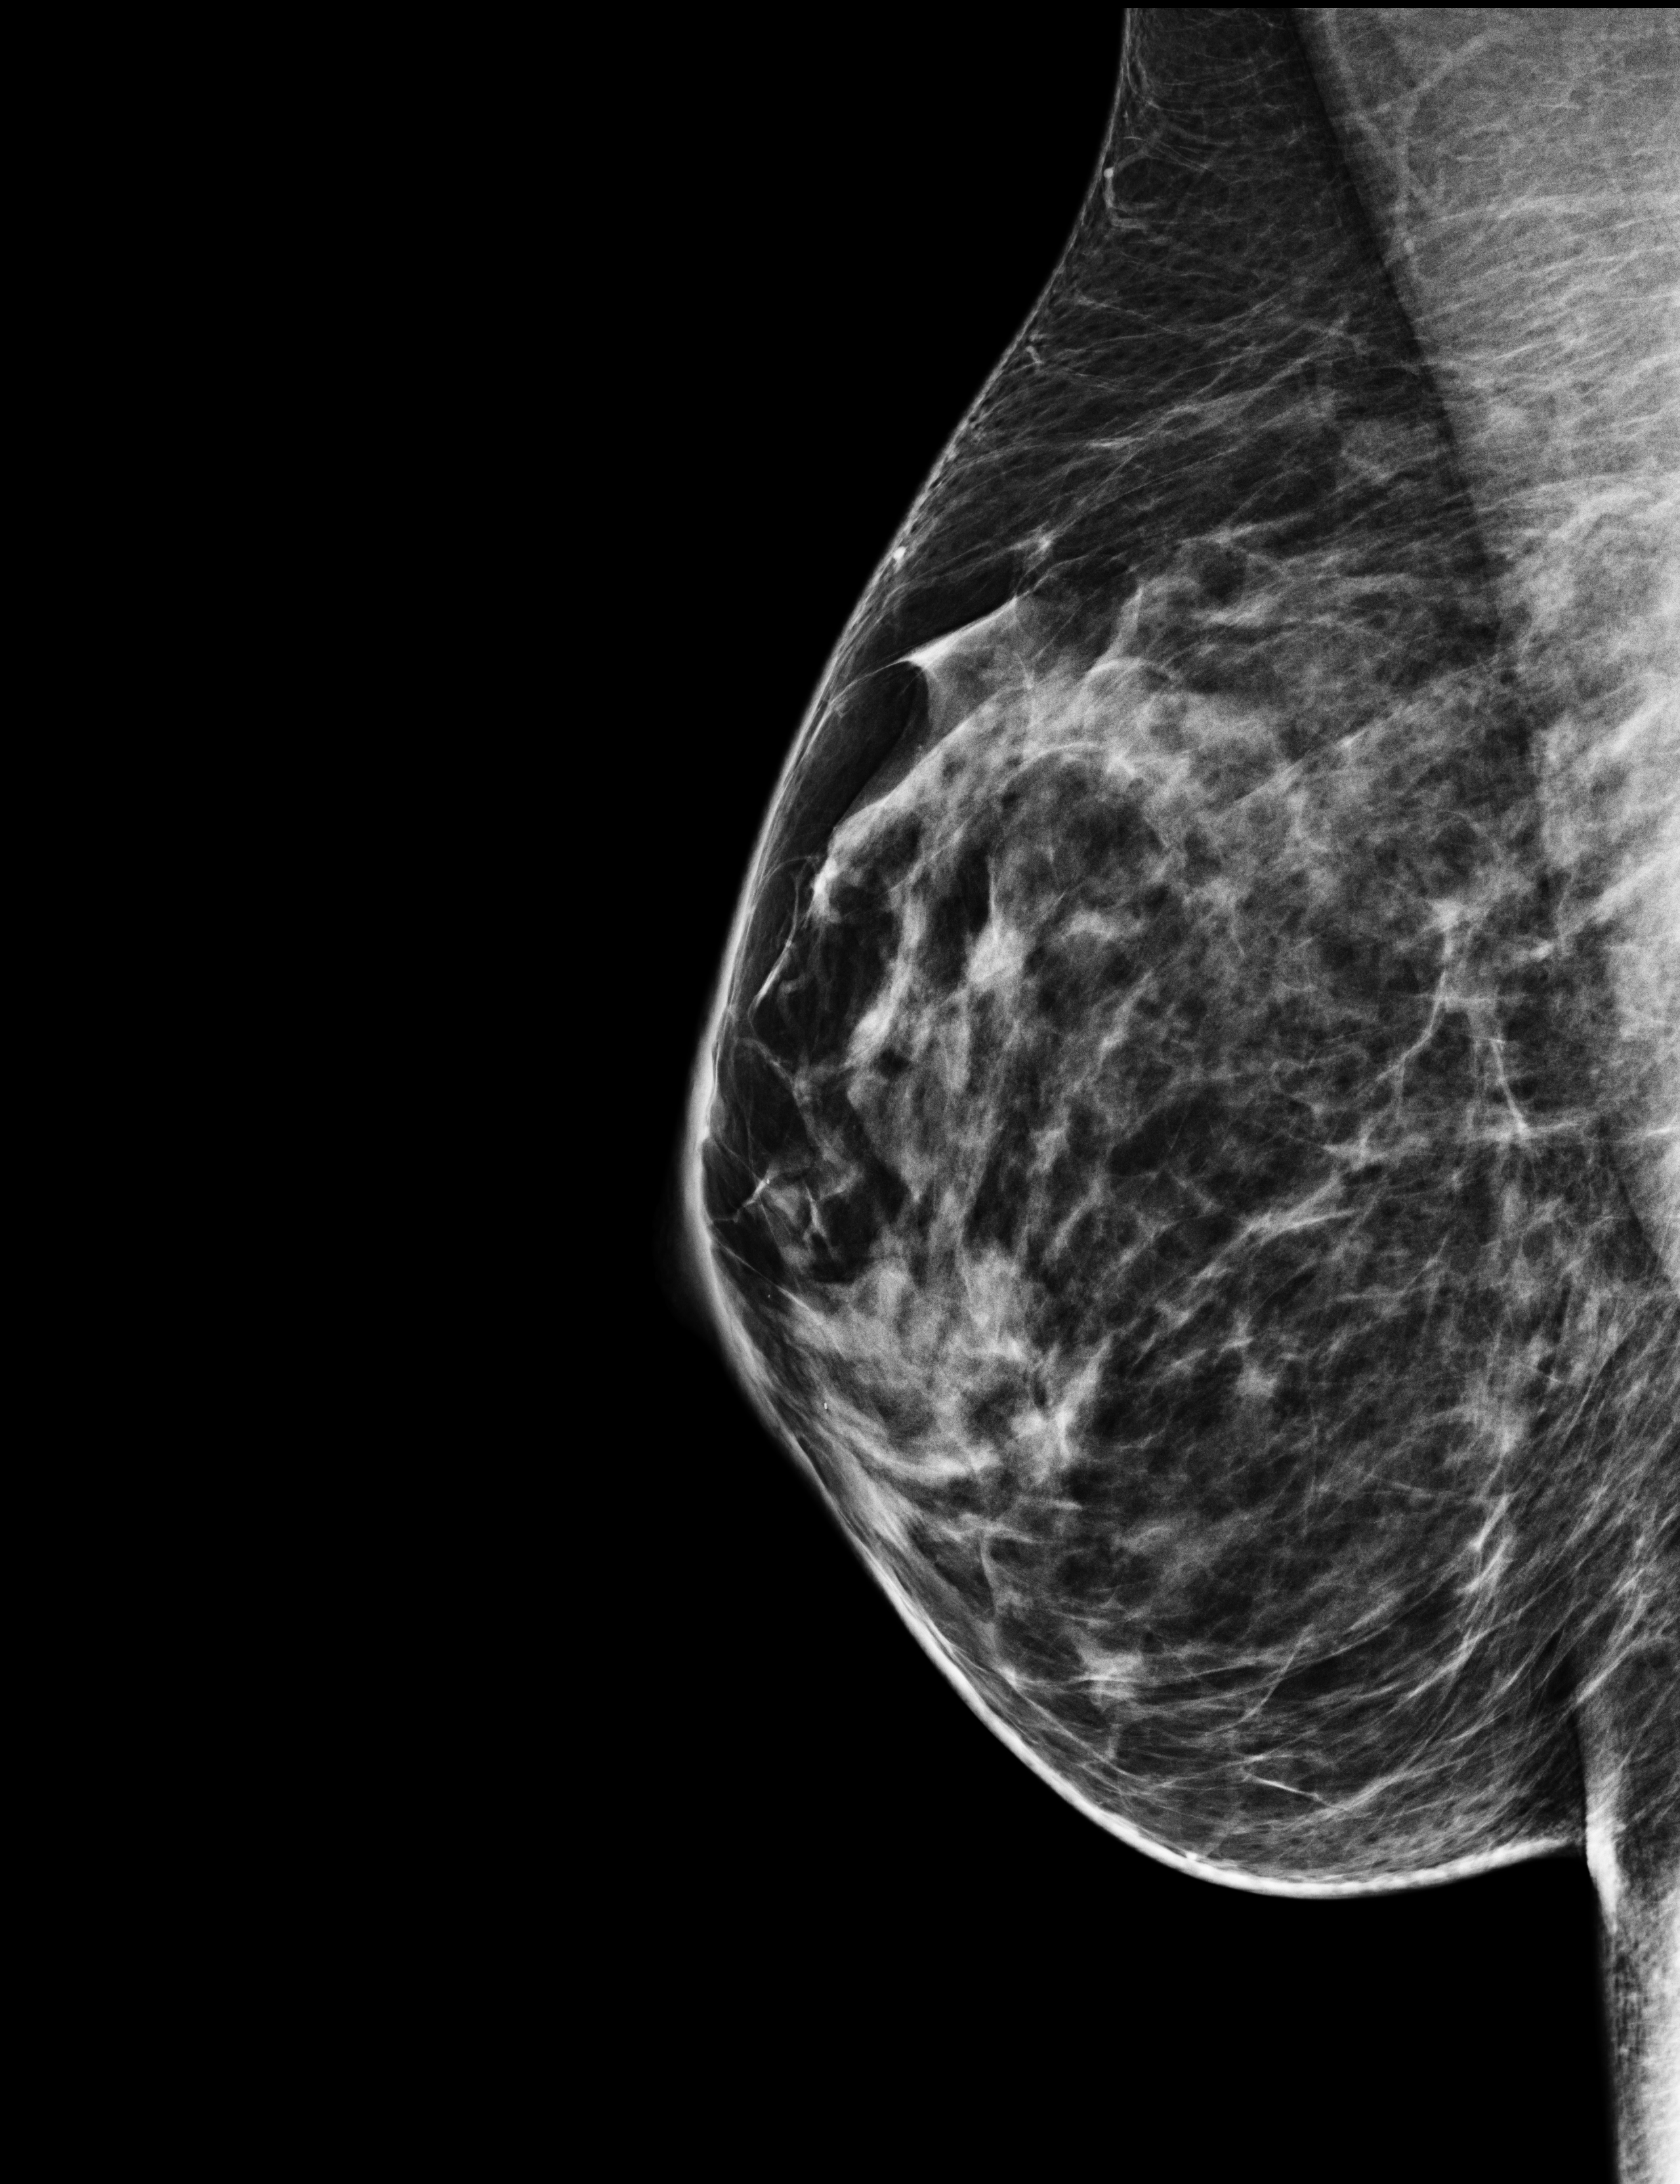
Annual screening mammography examination; compressed breast thickness 62 mm; system: Selenia Dimensions. Patient aged 45 years (female).
Image type: full-field digital mammogram. Breast: right. Projection: MLO view.